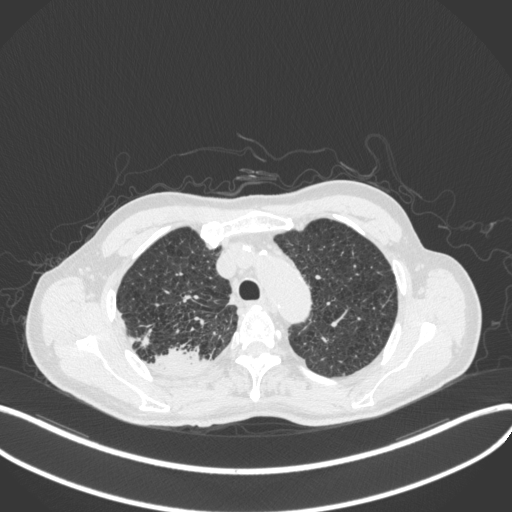
Chest CT, one axial slice; slice 345 of 423 in the series (ordered by position); 120 kVp; lung window (W 1500 / L -600 HU); 1 mm slice thickness; 512 × 512 image matrix, field of view 400 × 400 mm. Male patient, age 79 years. Case-level facts recorded for this patient, not image findings: clinical TNM (as recorded): T3 N0 M0.
Annotated regions visible in this slice (bounding box drawn by a radiologist):
- lung tumour (recorded histology: adenocarcinoma): bounding box <151,345,206,376> (left, top, right, bottom; pixels)